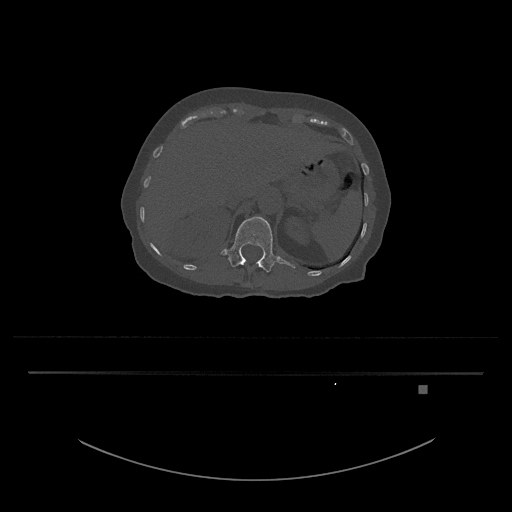
CT including the spine, one axial slice. Reconstruction kernel Br40s/3. Bone window (W 1800 / L 400 HU). 0.5 mm slice thickness. 512 × 512 image matrix, field of view 500 × 500 mm. Female patient, age 57 years. From the clinical record (not read from this slice): primary cancer: cervical.
Annotated regions visible in this slice (semi-automatically segmented with operator editing):
- L1 vertebra: bounding box [x1, y1, x2, y2] px = [220, 216, 296, 273]